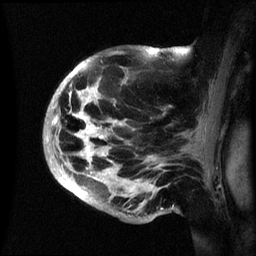
Breast MRI (dynamic contrast-enhanced), one sagittal slice. Slice 43 of 60 in the series (ordered by position). Dynamic contrast-enhanced series, image 2 of 3 at this slice position (ordered by acquisition). 1.5 T. TE 4.2 ms, TR 8.4 ms. 2.4 mm slice thickness. 256 × 256 image matrix, field of view 230 × 230 mm. Patient: female, 48 years.
Structures marked on this image (semi-automatically segmented with operator editing):
- analysis volume of interest (the breast-tissue region the enhancement analysis was run in; not a lesion): bounding box [x1, y1, x2, y2] px = [44, 47, 191, 222]
- tumour enhancement mask (voxels above the 70 % enhancement threshold inside the analysis volume of interest): [52, 48, 157, 192]